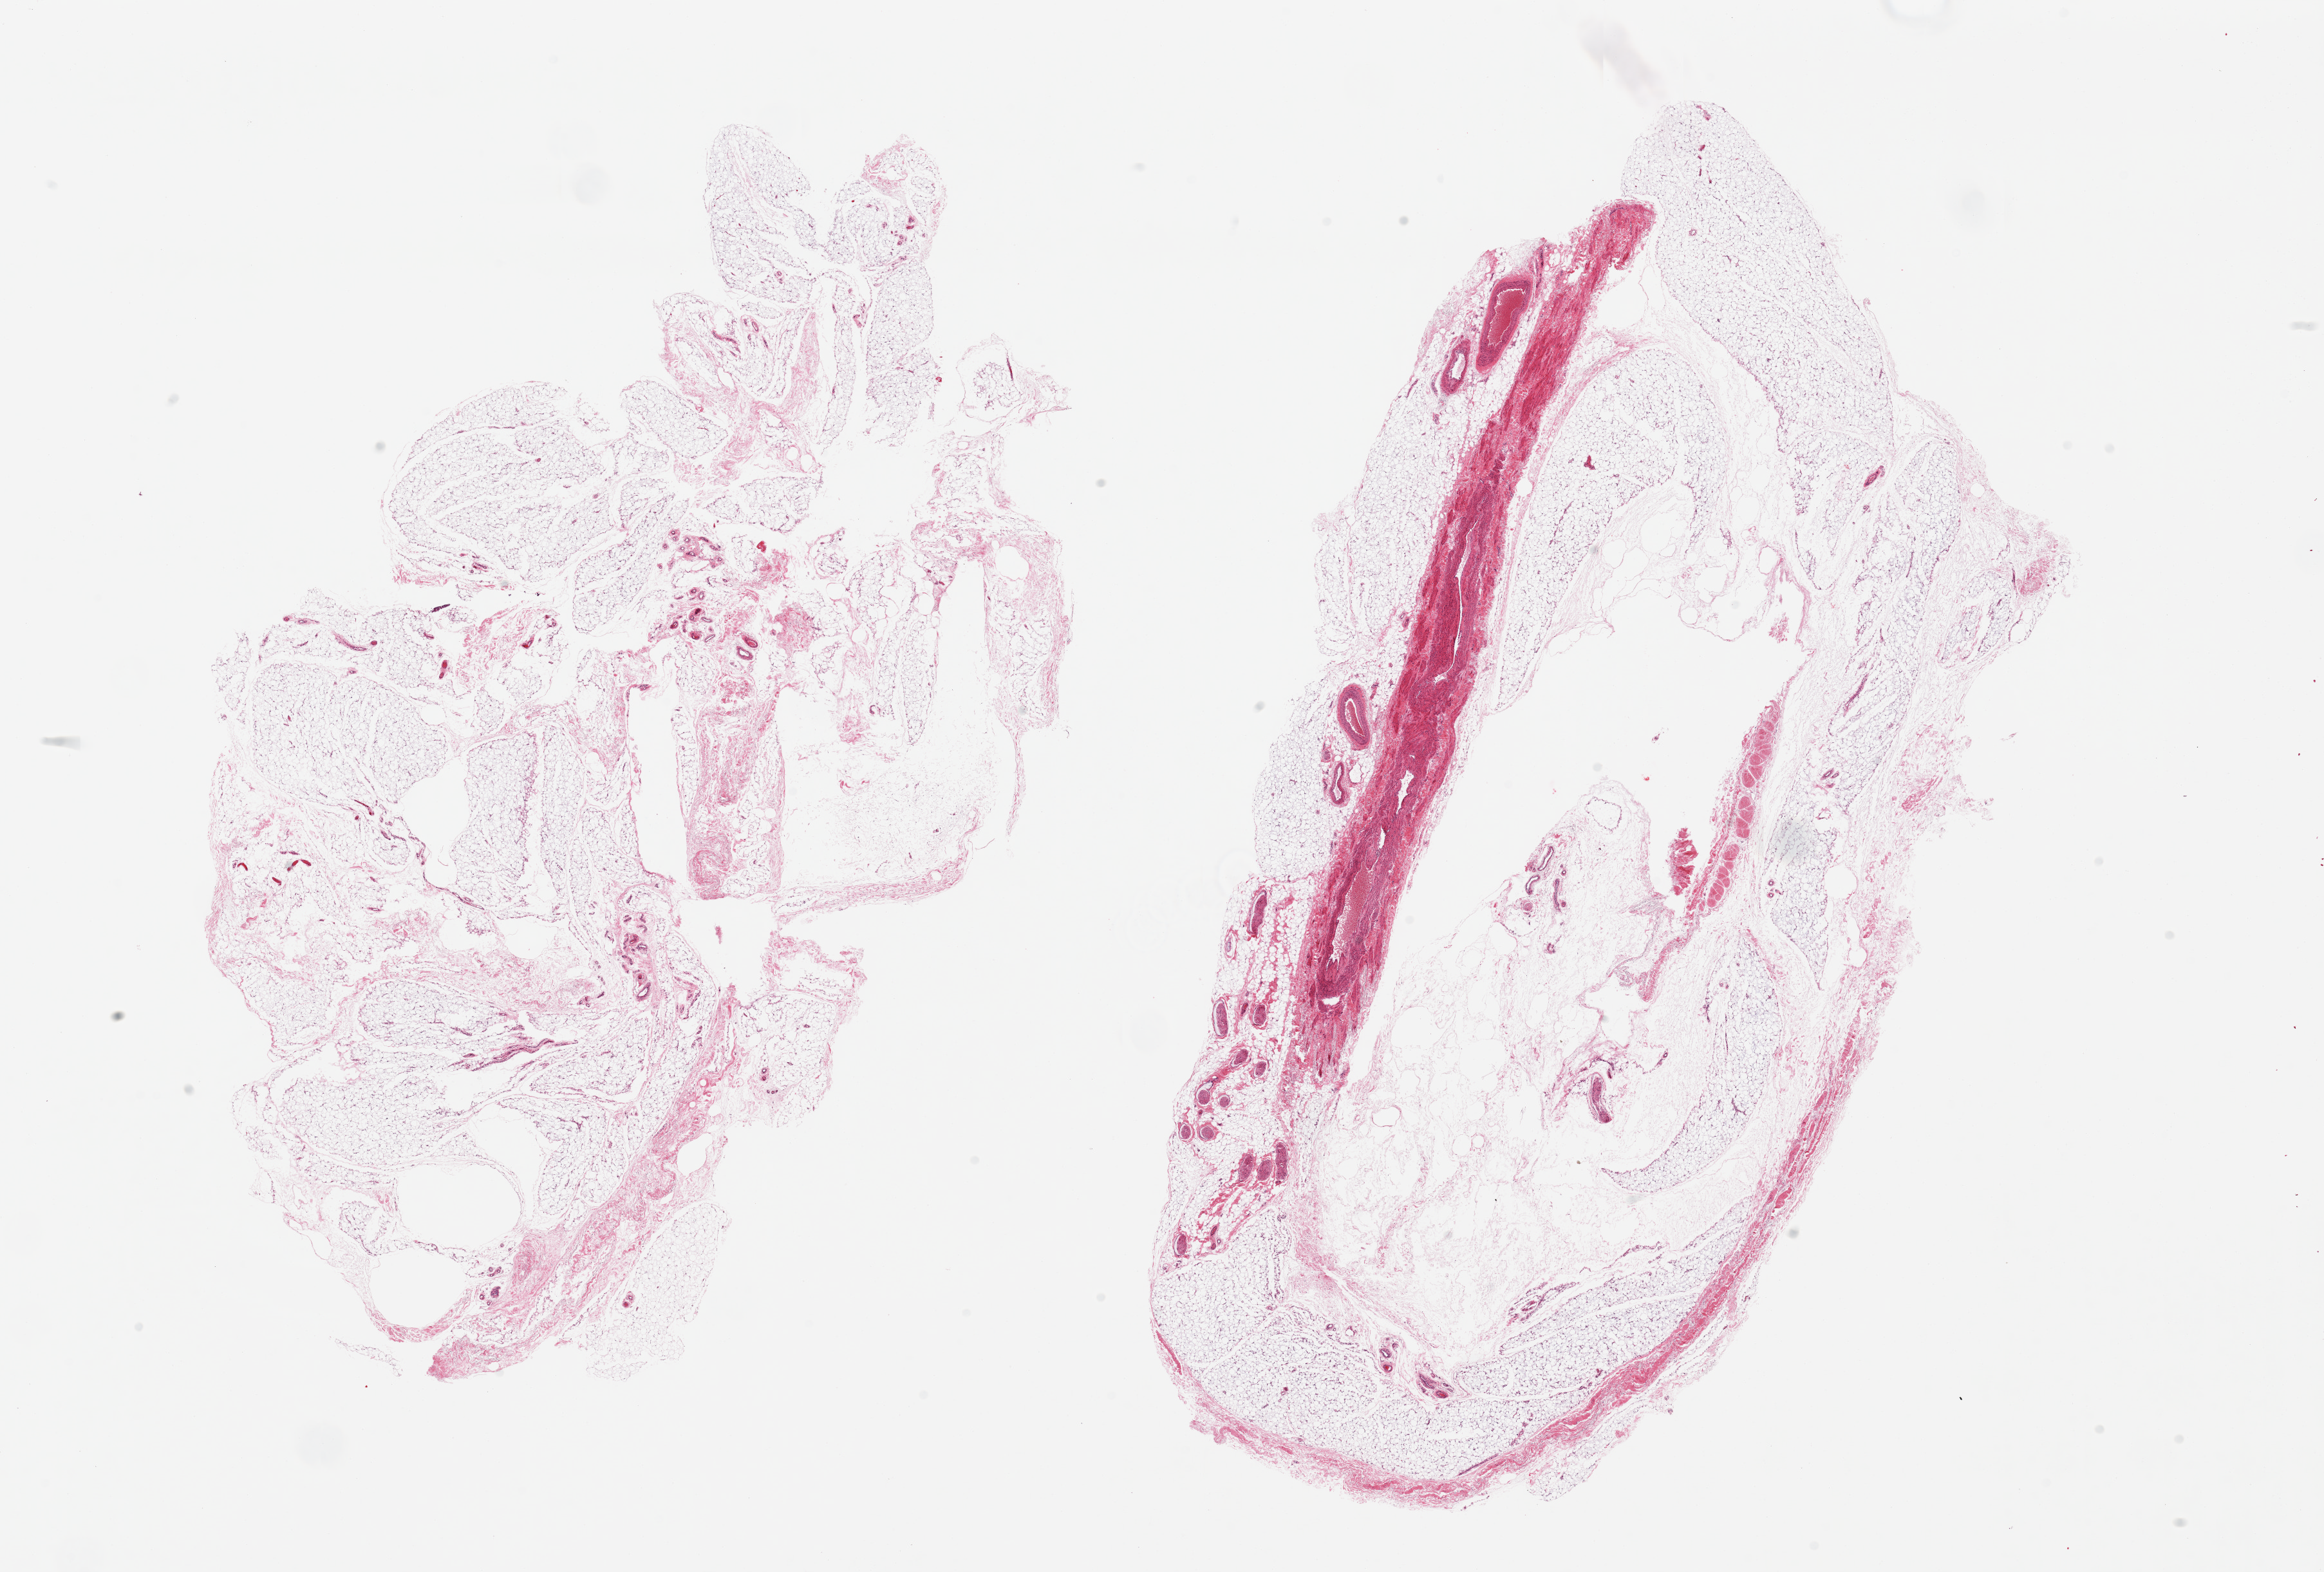
Whole-slide image, haematoxylin and eosin stain, shown as a low-resolution overview of the whole scanned area (about 28.5 x 19.3 mm). PAXgene-fixed, paraffin-embedded tissue. Section of adipose tissue (target tissue). Donor tissue sample.
Review note (as recorded): 2 pieces, ~10% prominent vessel/fascia.